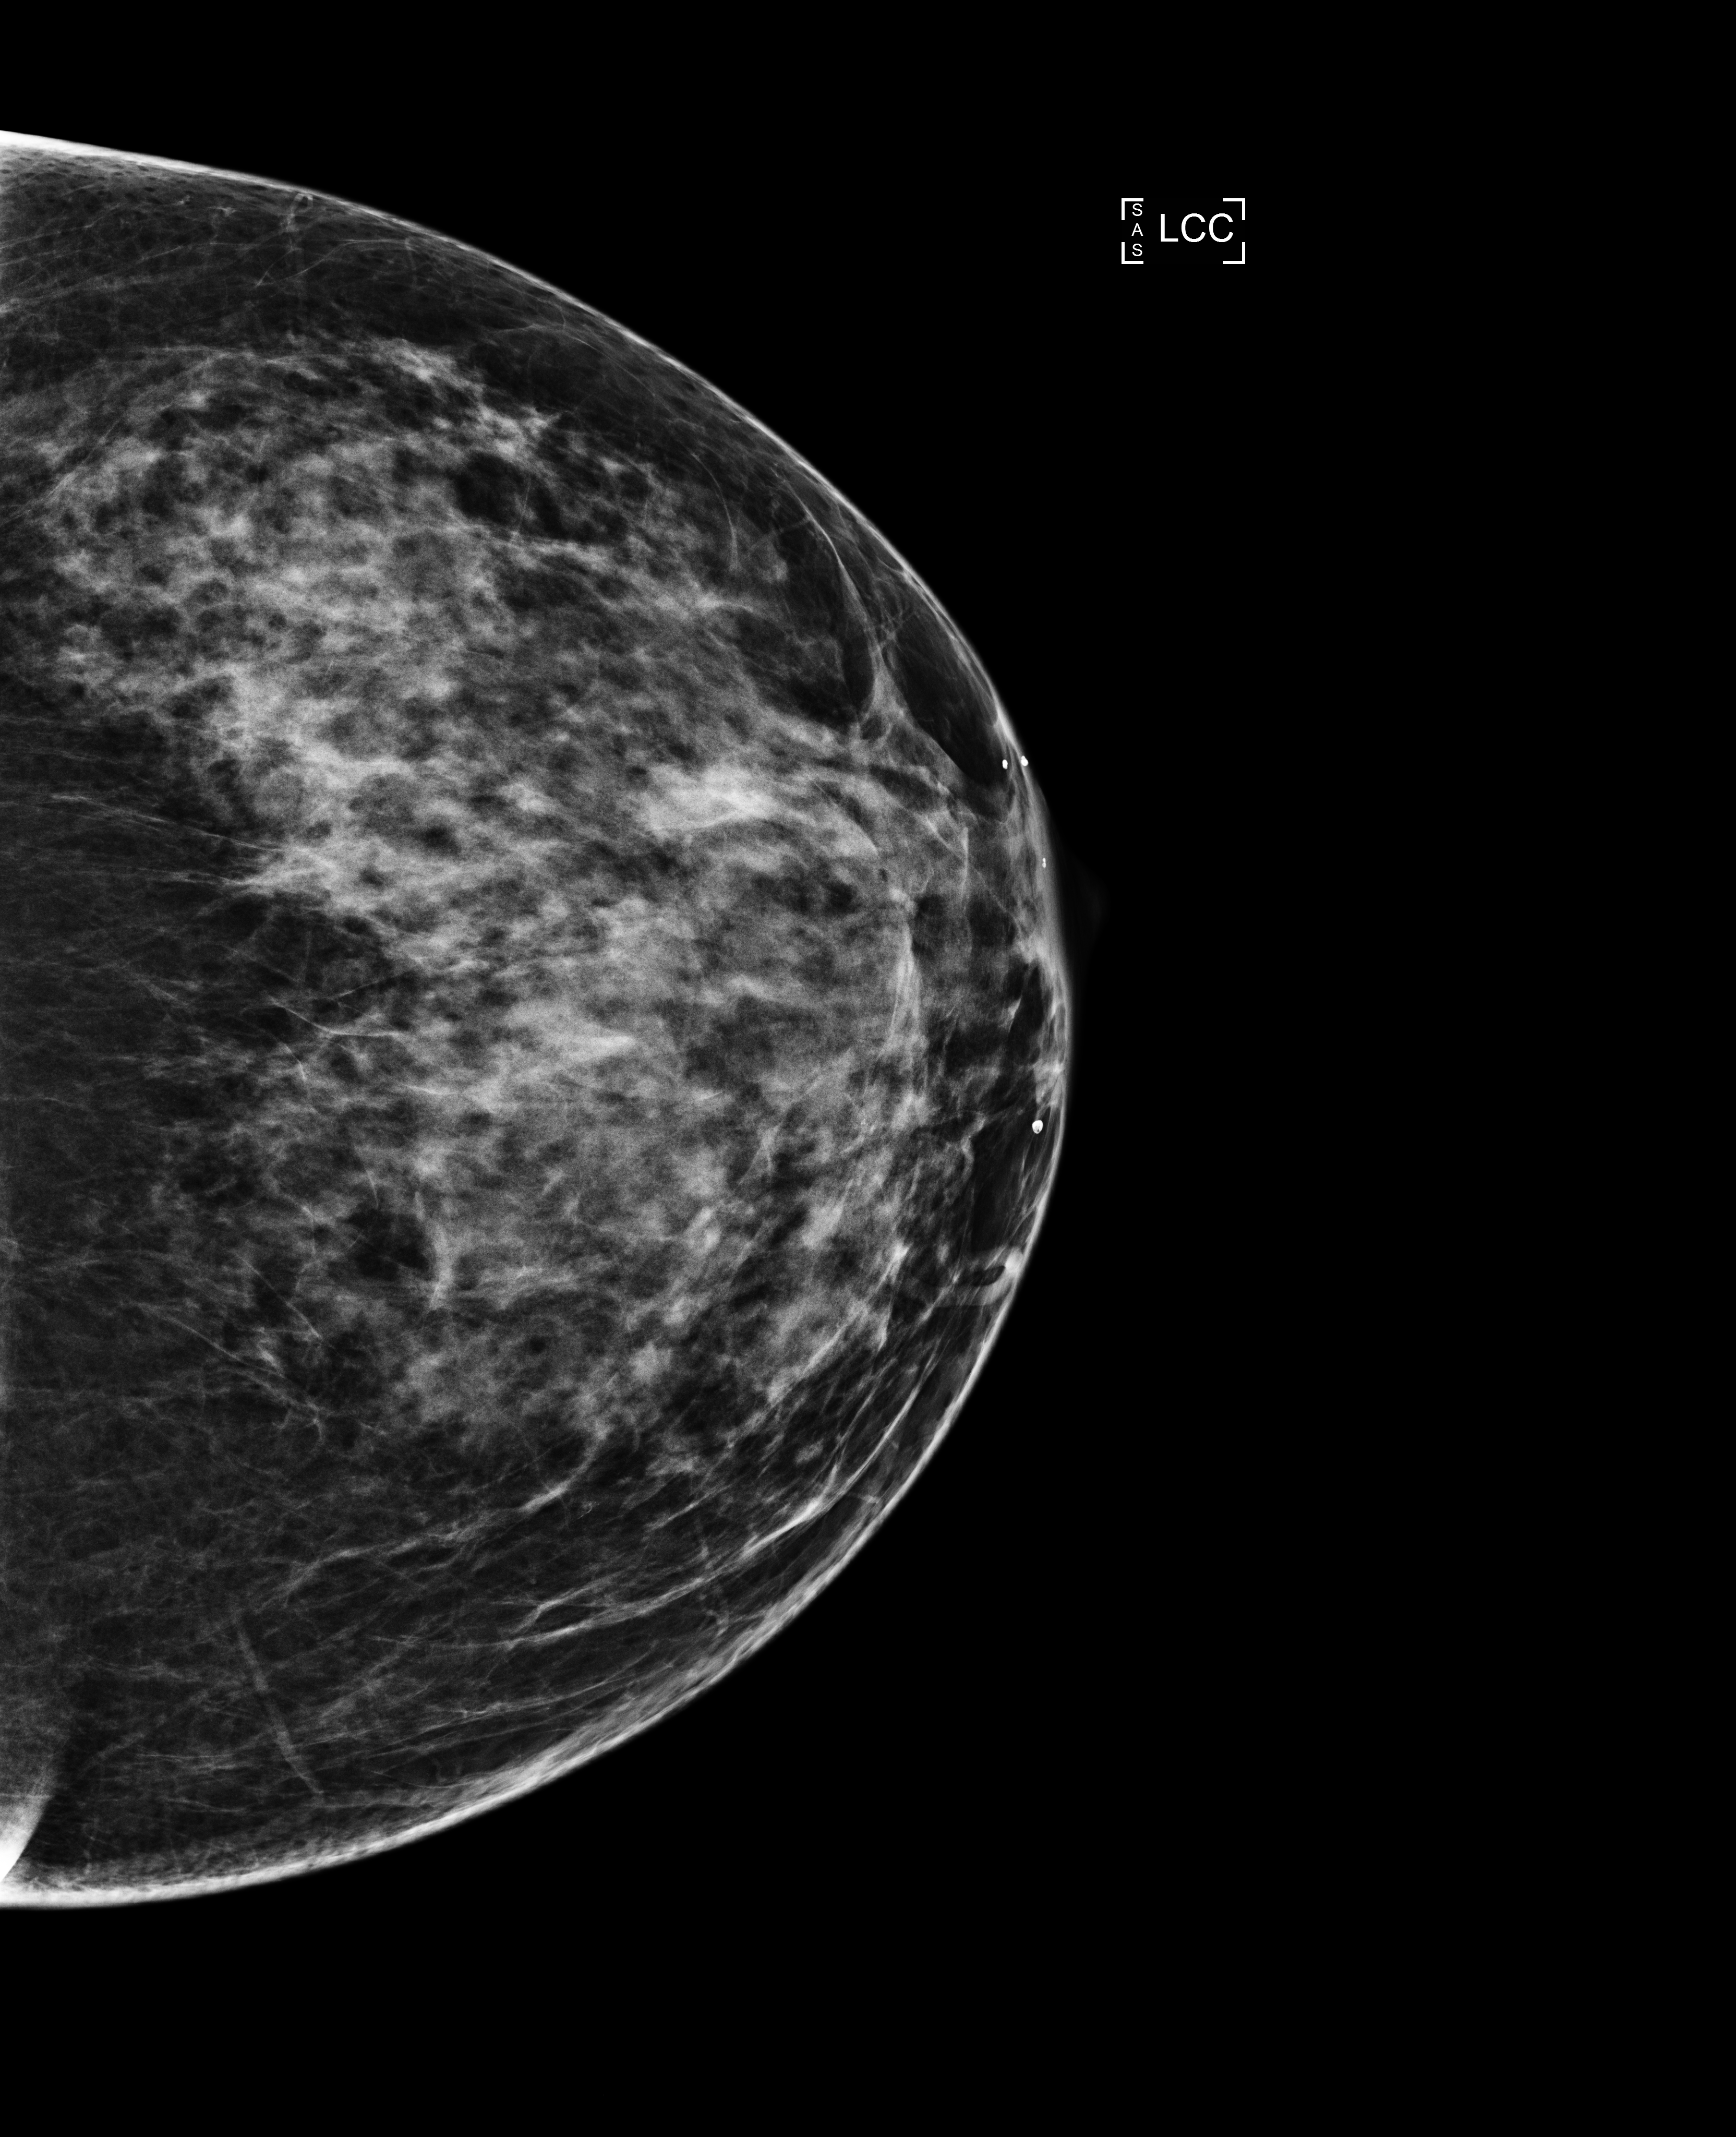
Annual screening mammography examination, compressed breast thickness 66 mm. Patient: female, 44 years.
Image type: full-field digital mammogram. Breast: left. Projection: craniocaudal (CC) view.